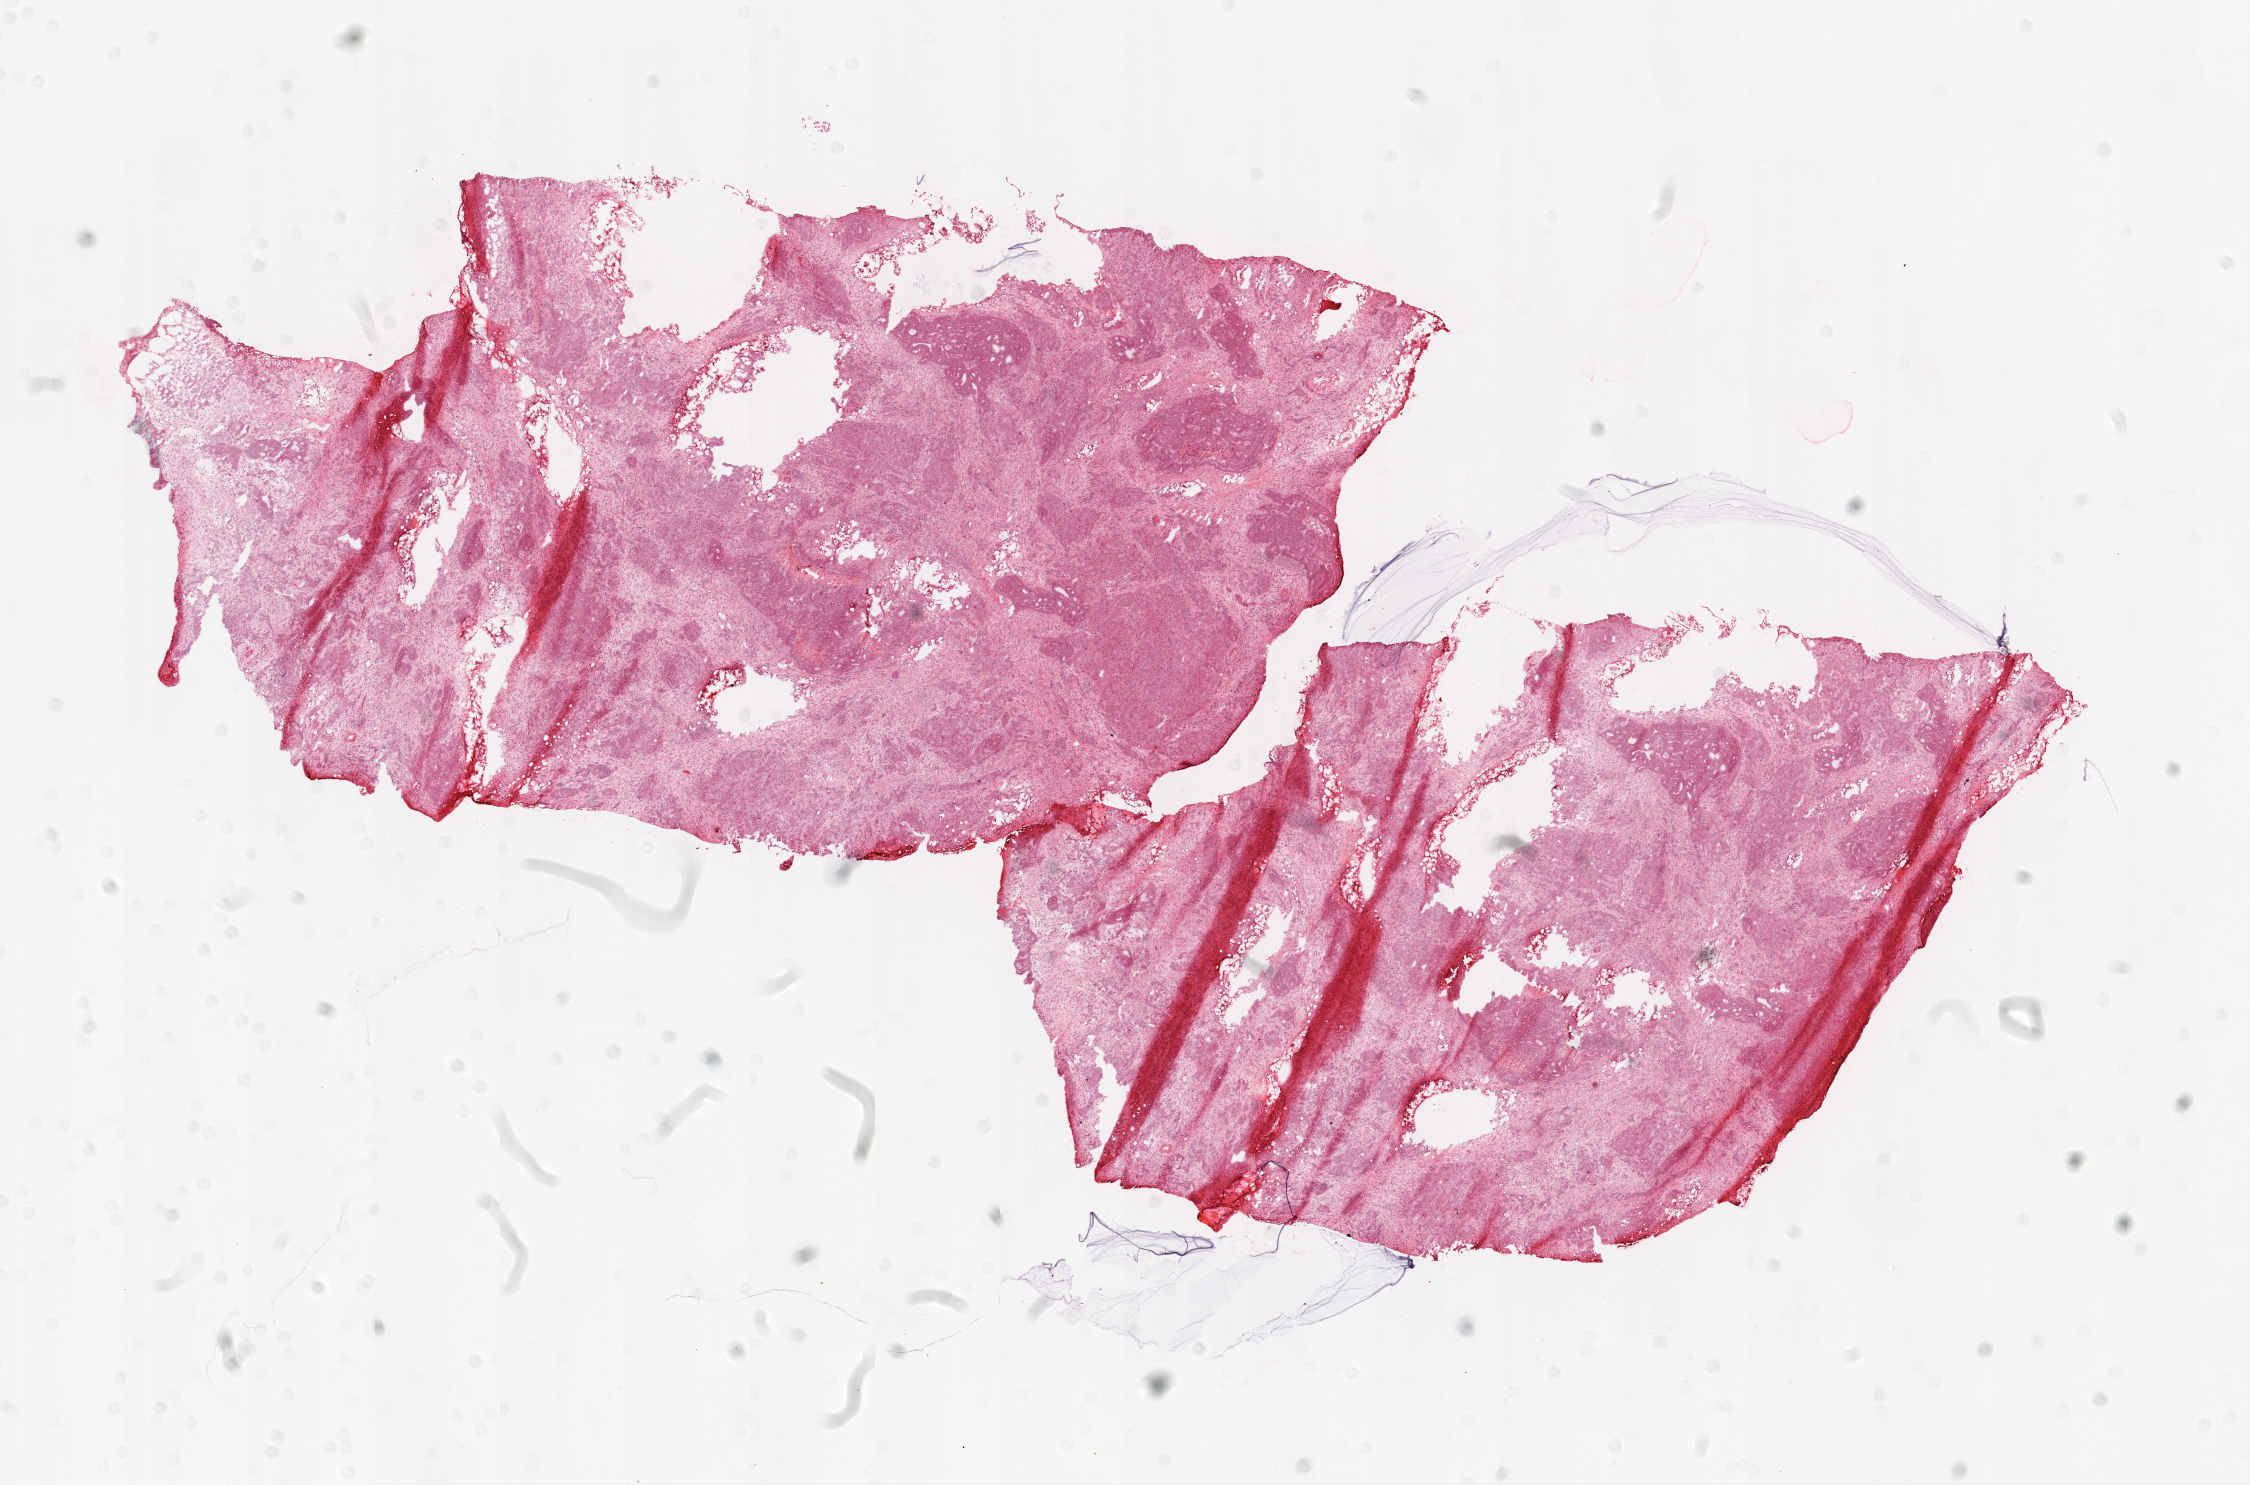
H&E whole-slide image, shown as a low-resolution overview of the whole scanned area (about 18.1 x 11.9 mm, slide scanned at 20x). Frozen section. Primary tumour sample from the ovary. Female patient; age at initial diagnosis 49 years. Histologic grade: G2 (moderately differentiated). Slide review estimates, as recorded: tumour cells 60%, tumour nuclei 75%, normal cells 0%, stromal cells 37%, necrosis 3%. Inflammatory infiltration, as recorded: lymphocyte infiltration 2%.
FIGO stage: IV. Pathologic diagnosis: Serous cystadenocarcinoma, NOS. Laterality: bilateral.